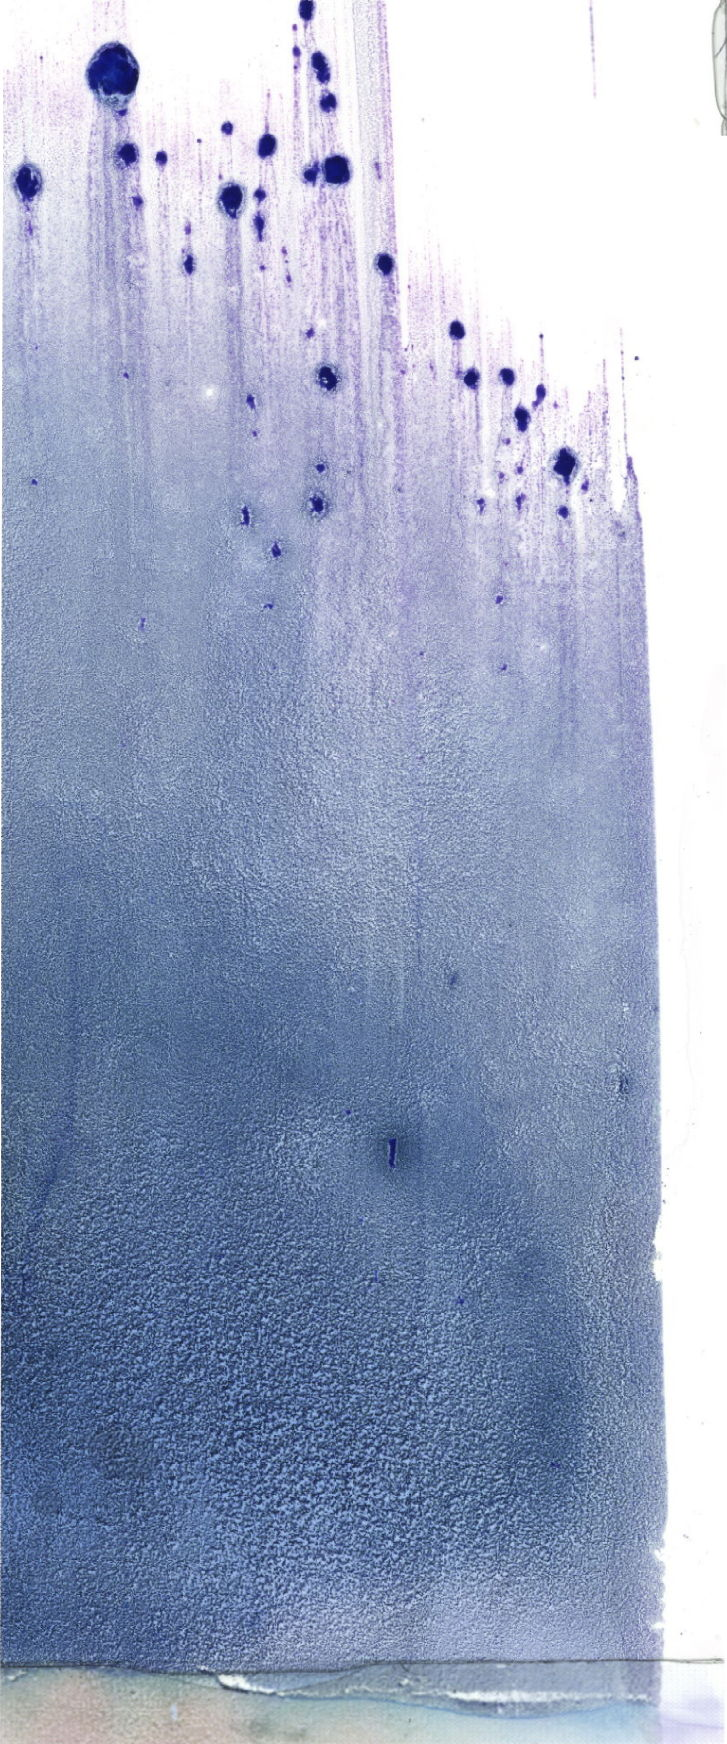
Bone marrow aspirate smear, May-Grünwald-Giemsa (MGG) stain, whole-slide image, shown as a low-resolution overview of the whole scanned area (about 20.6 x 49.4 mm). Patient sex: male.
Diagnosis: Acute Monocytic Leukemia.